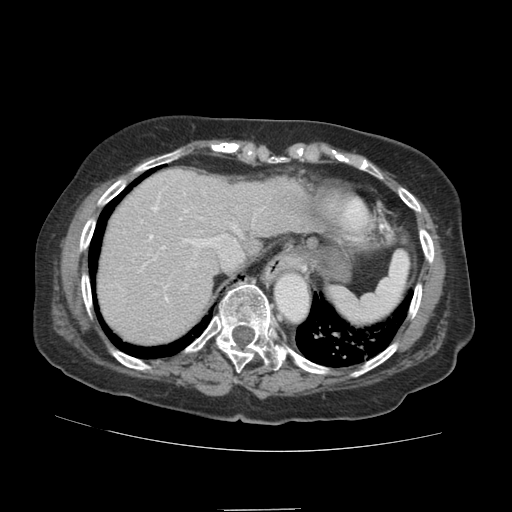
Contrast-enhanced abdominal CT (liver protocol), one axial slice. Slice 73 of 89 in the series (ordered by position). Reconstruction kernel STANDARD. Soft-tissue window (W 400 / L 40 HU). 2.5 mm slice thickness. 512 × 512 image matrix, field of view 360 × 360 mm. Case-level facts recorded for this patient, not image findings: diagnosis: hepatocellular carcinoma (patient treated with transarterial chemoembolisation; whether this scan precedes or follows treatment is not stated here); TNM stage (as recorded): Stage-II; Child-Pugh class: A; tumour nodularity: multinodular; tumour size: 4 cm.
Structures marked on this image (semi-automatic segmentation, software-assisted and operator-edited):
- abdominal aorta: bounding box <276,276,309,319> (left, top, right, bottom; pixels)
- liver parenchyma outside the tumour (the mass and vessels are separate outlines, so this box may not span the whole liver): <98,168,316,344>
- liver vessels: <139,195,239,301>